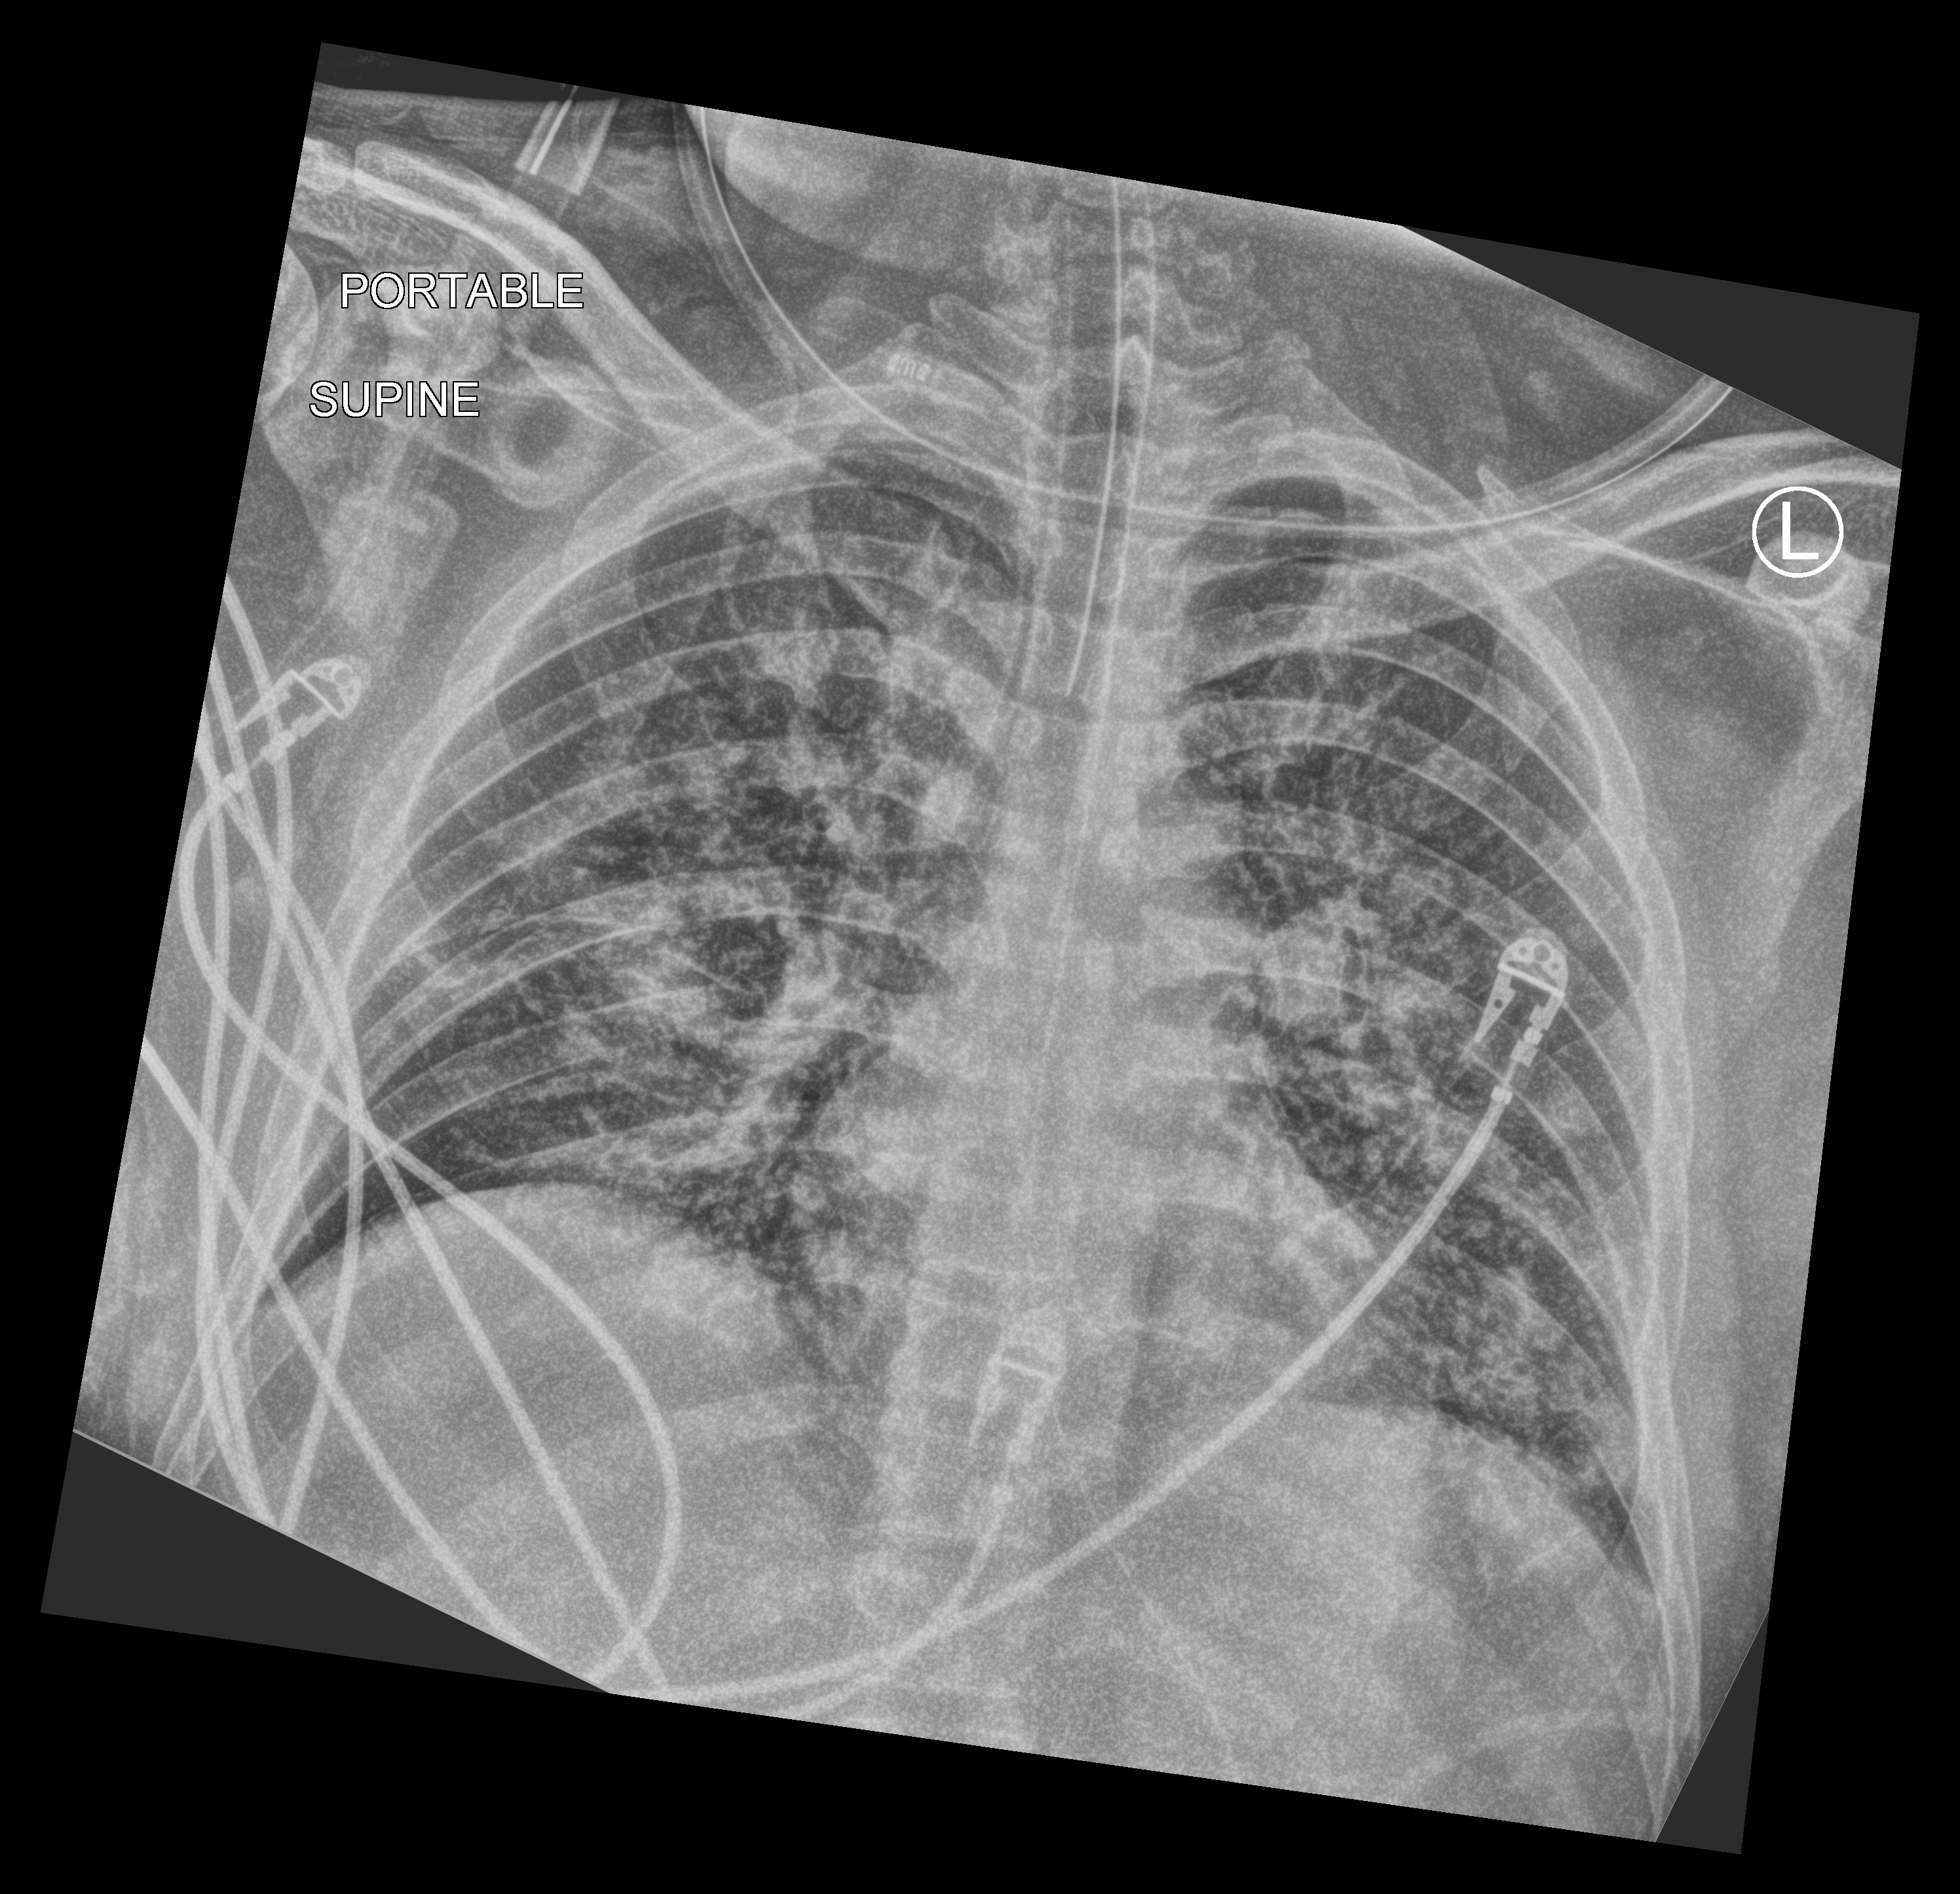
Bedside chest radiograph (computed radiography), anteroposterior (AP) projection. Adult patient hospitalised with COVID-19, age 18–59 years.
Hospital-stay facts (about this admission, not read from this image; timing relative to this image not recorded): COPD (admission record): no; smoking status (admission record): never; mechanically ventilated during this hospital stay: yes.